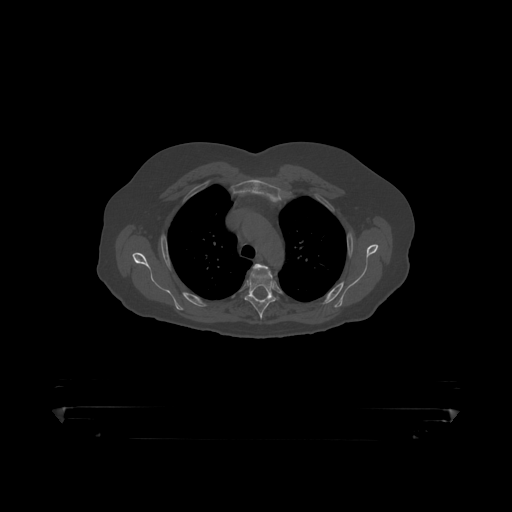
CT including the spine, one axial slice; slice 340 of 390 in the series (ordered by position); reconstruction kernel STANDARD; 120 kVp; bone window (W 1800 / L 400 HU); 1.25 mm slice thickness; 512 × 512 image matrix. Patient: male, 60 years. Case-level facts recorded for this patient, not image findings: primary cancer: prostate.
Structures marked on this image (semi-automatic segmentation, software-assisted and operator-edited):
- T3 vertebra: bounding box (x1, y1, x2, y2) in pixels: (259, 267, 266, 272)
- T4 vertebra: (245, 264, 280, 319)